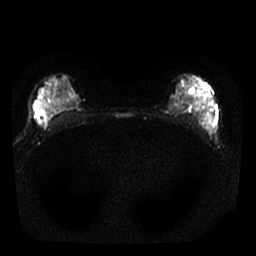
Breast MRI, one axial slice; position 16 of 25 along the scan axis; diffusion-weighted series; image 2 of 4 stored at this slice position (different b-values; order by instance number); 1.5 T; 256 × 256 image matrix, field of view 290 × 290 mm. Female patient.
Outlined on this slice (expert manual segmentation):
- tumour on diffusion-weighted imaging: bounding box <37,106,63,127> (left, top, right, bottom; pixels)